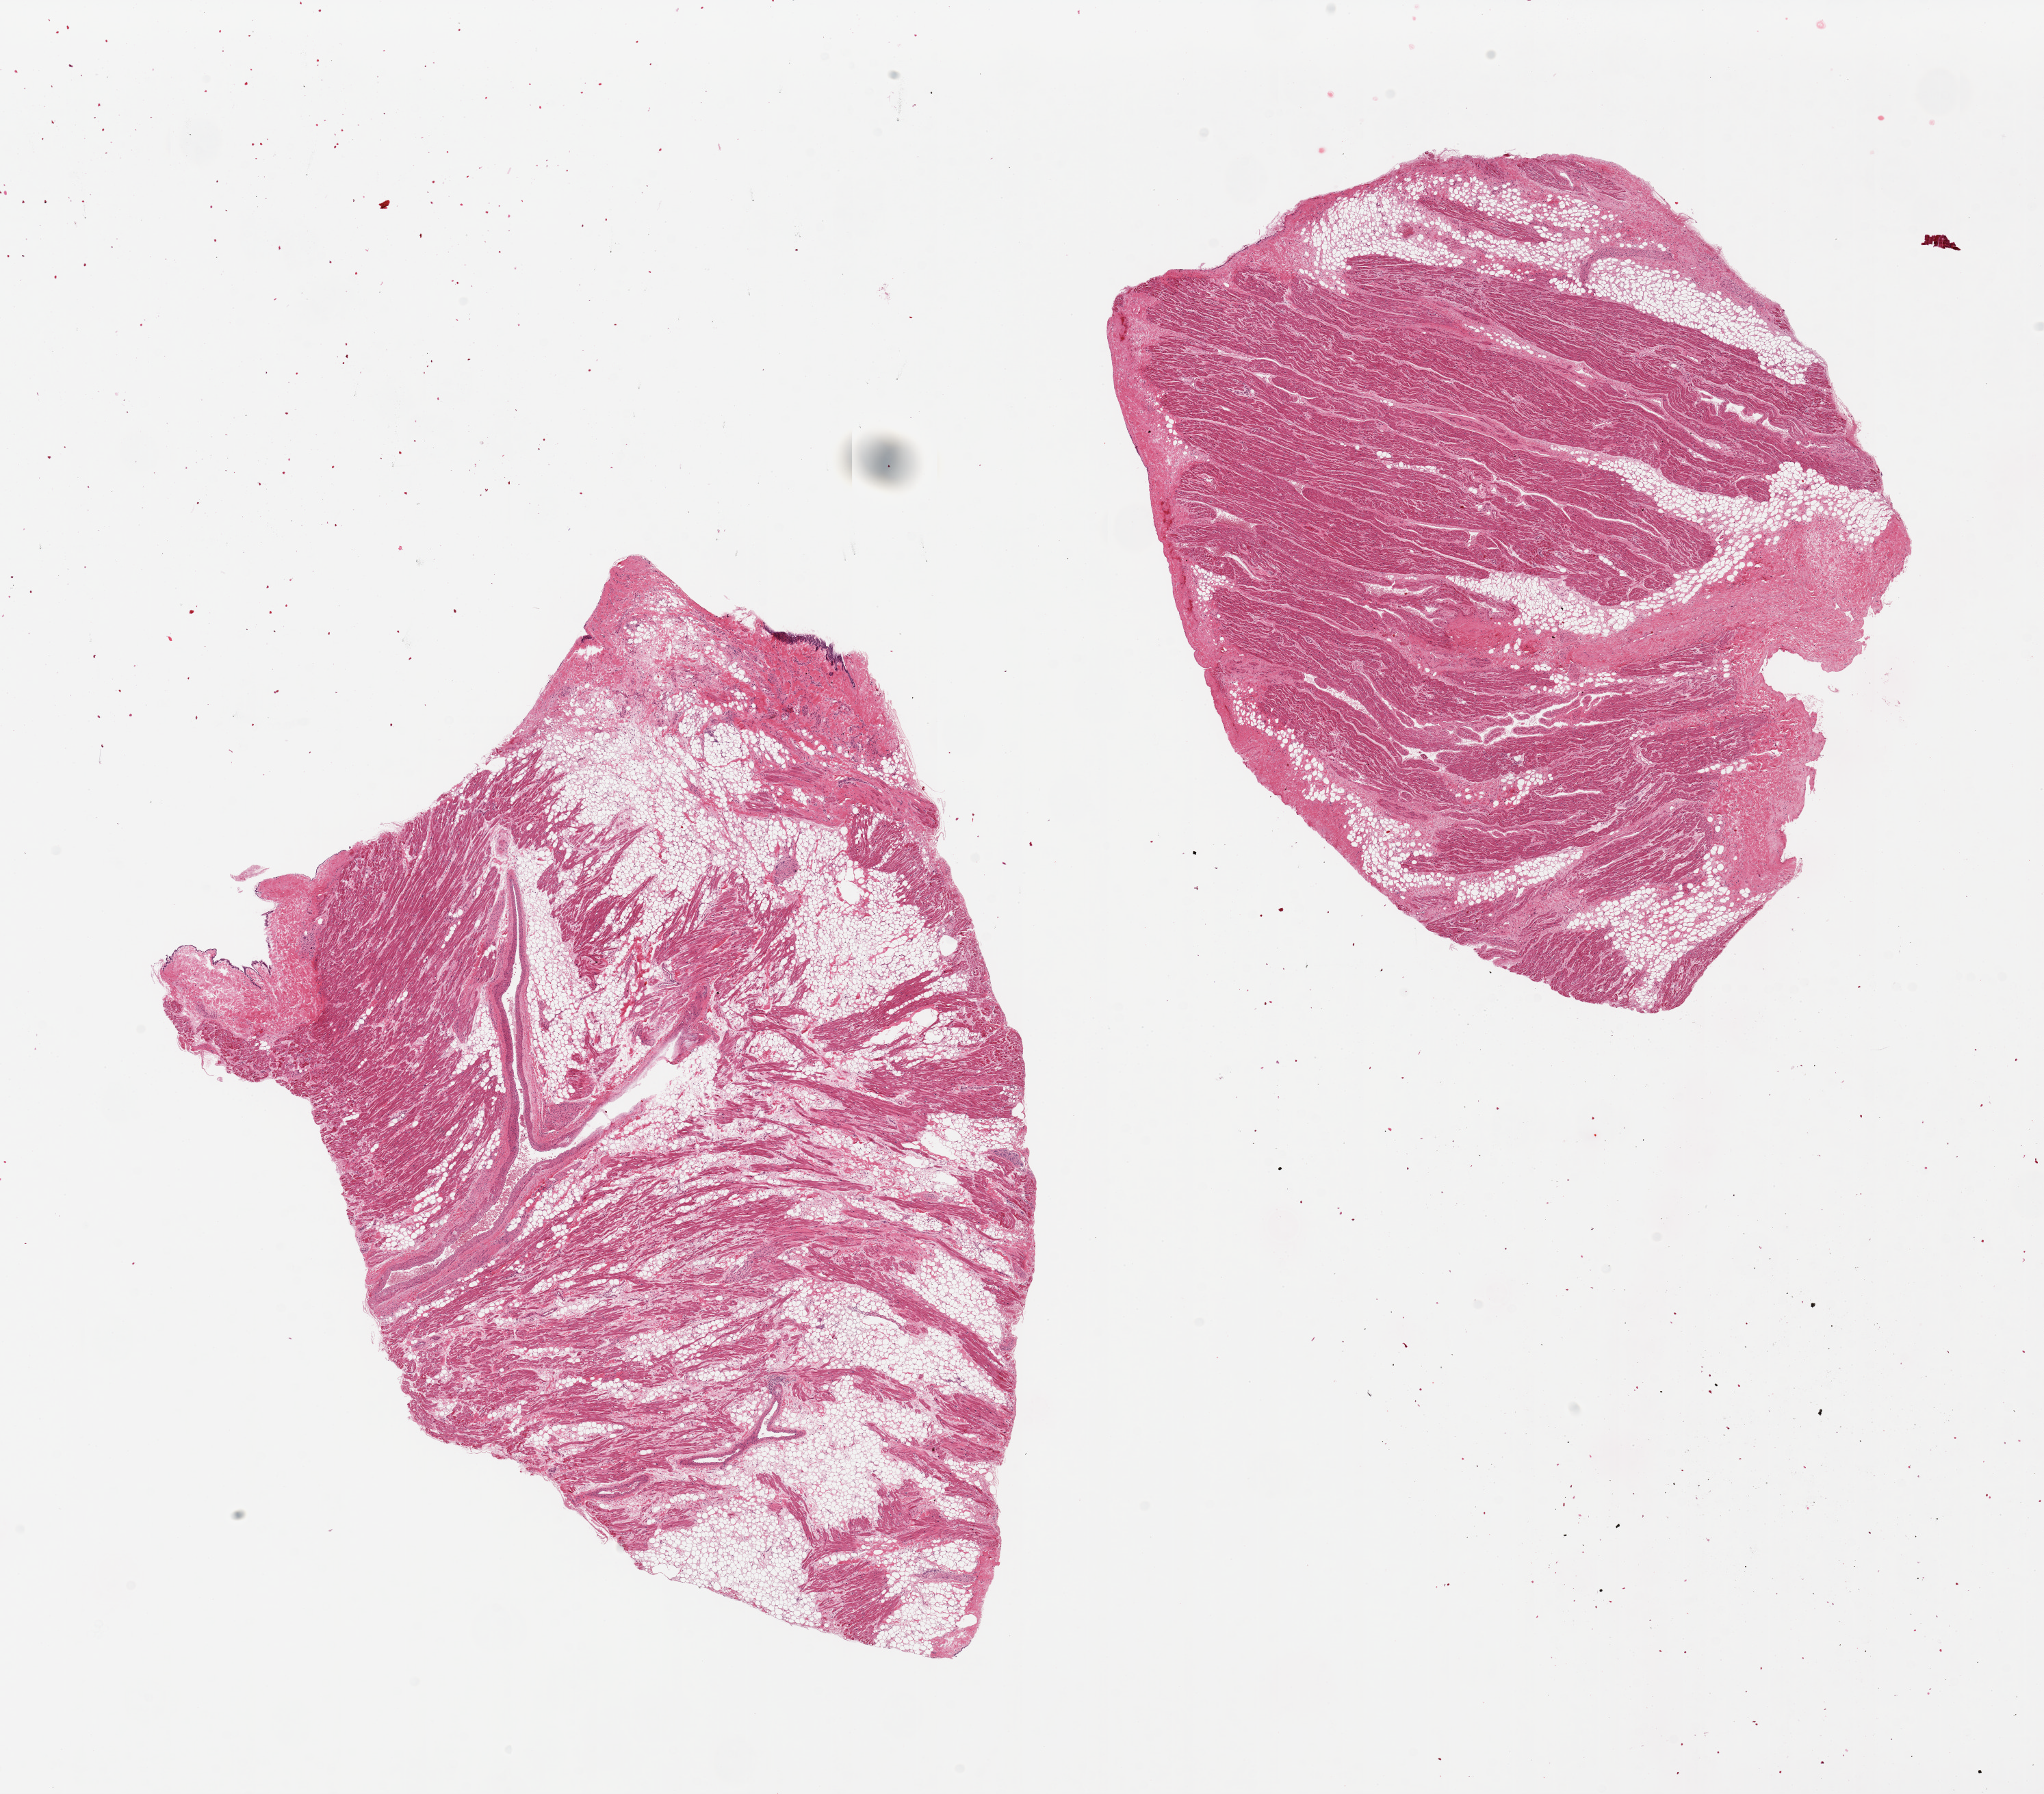
Whole-slide image, H&E stain — low-resolution overview of the scanned area, about 23.6 x 20.7 mm; PAXgene-fixed paraffin-embedded (PFPE) section; target tissue: auricular appendage; donor tissue sample. Donor sex: male.
Review note (as recorded): 2 pieces, not omentum as originally labeled; appears to represent atrial appendage specimen with interstitial and patchy fibrosis.